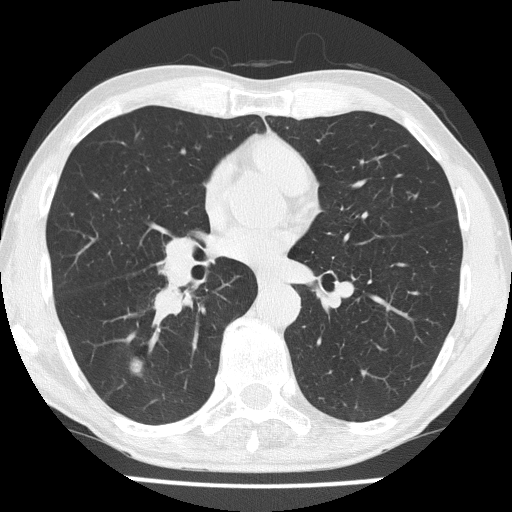
Low-dose screening chest CT, one axial slice. Position 85 of 186 along the scan axis. 120 kVp. Lung window (W 1500 / L -600 HU). 512 × 512 image matrix, field of view 328 × 328 mm.
Annotated regions visible in this slice (manually delineated by an expert):
- lesion 1 (tumor, lower lobe of right lung): bounding box <130,357,144,374> (left, top, right, bottom; pixels)